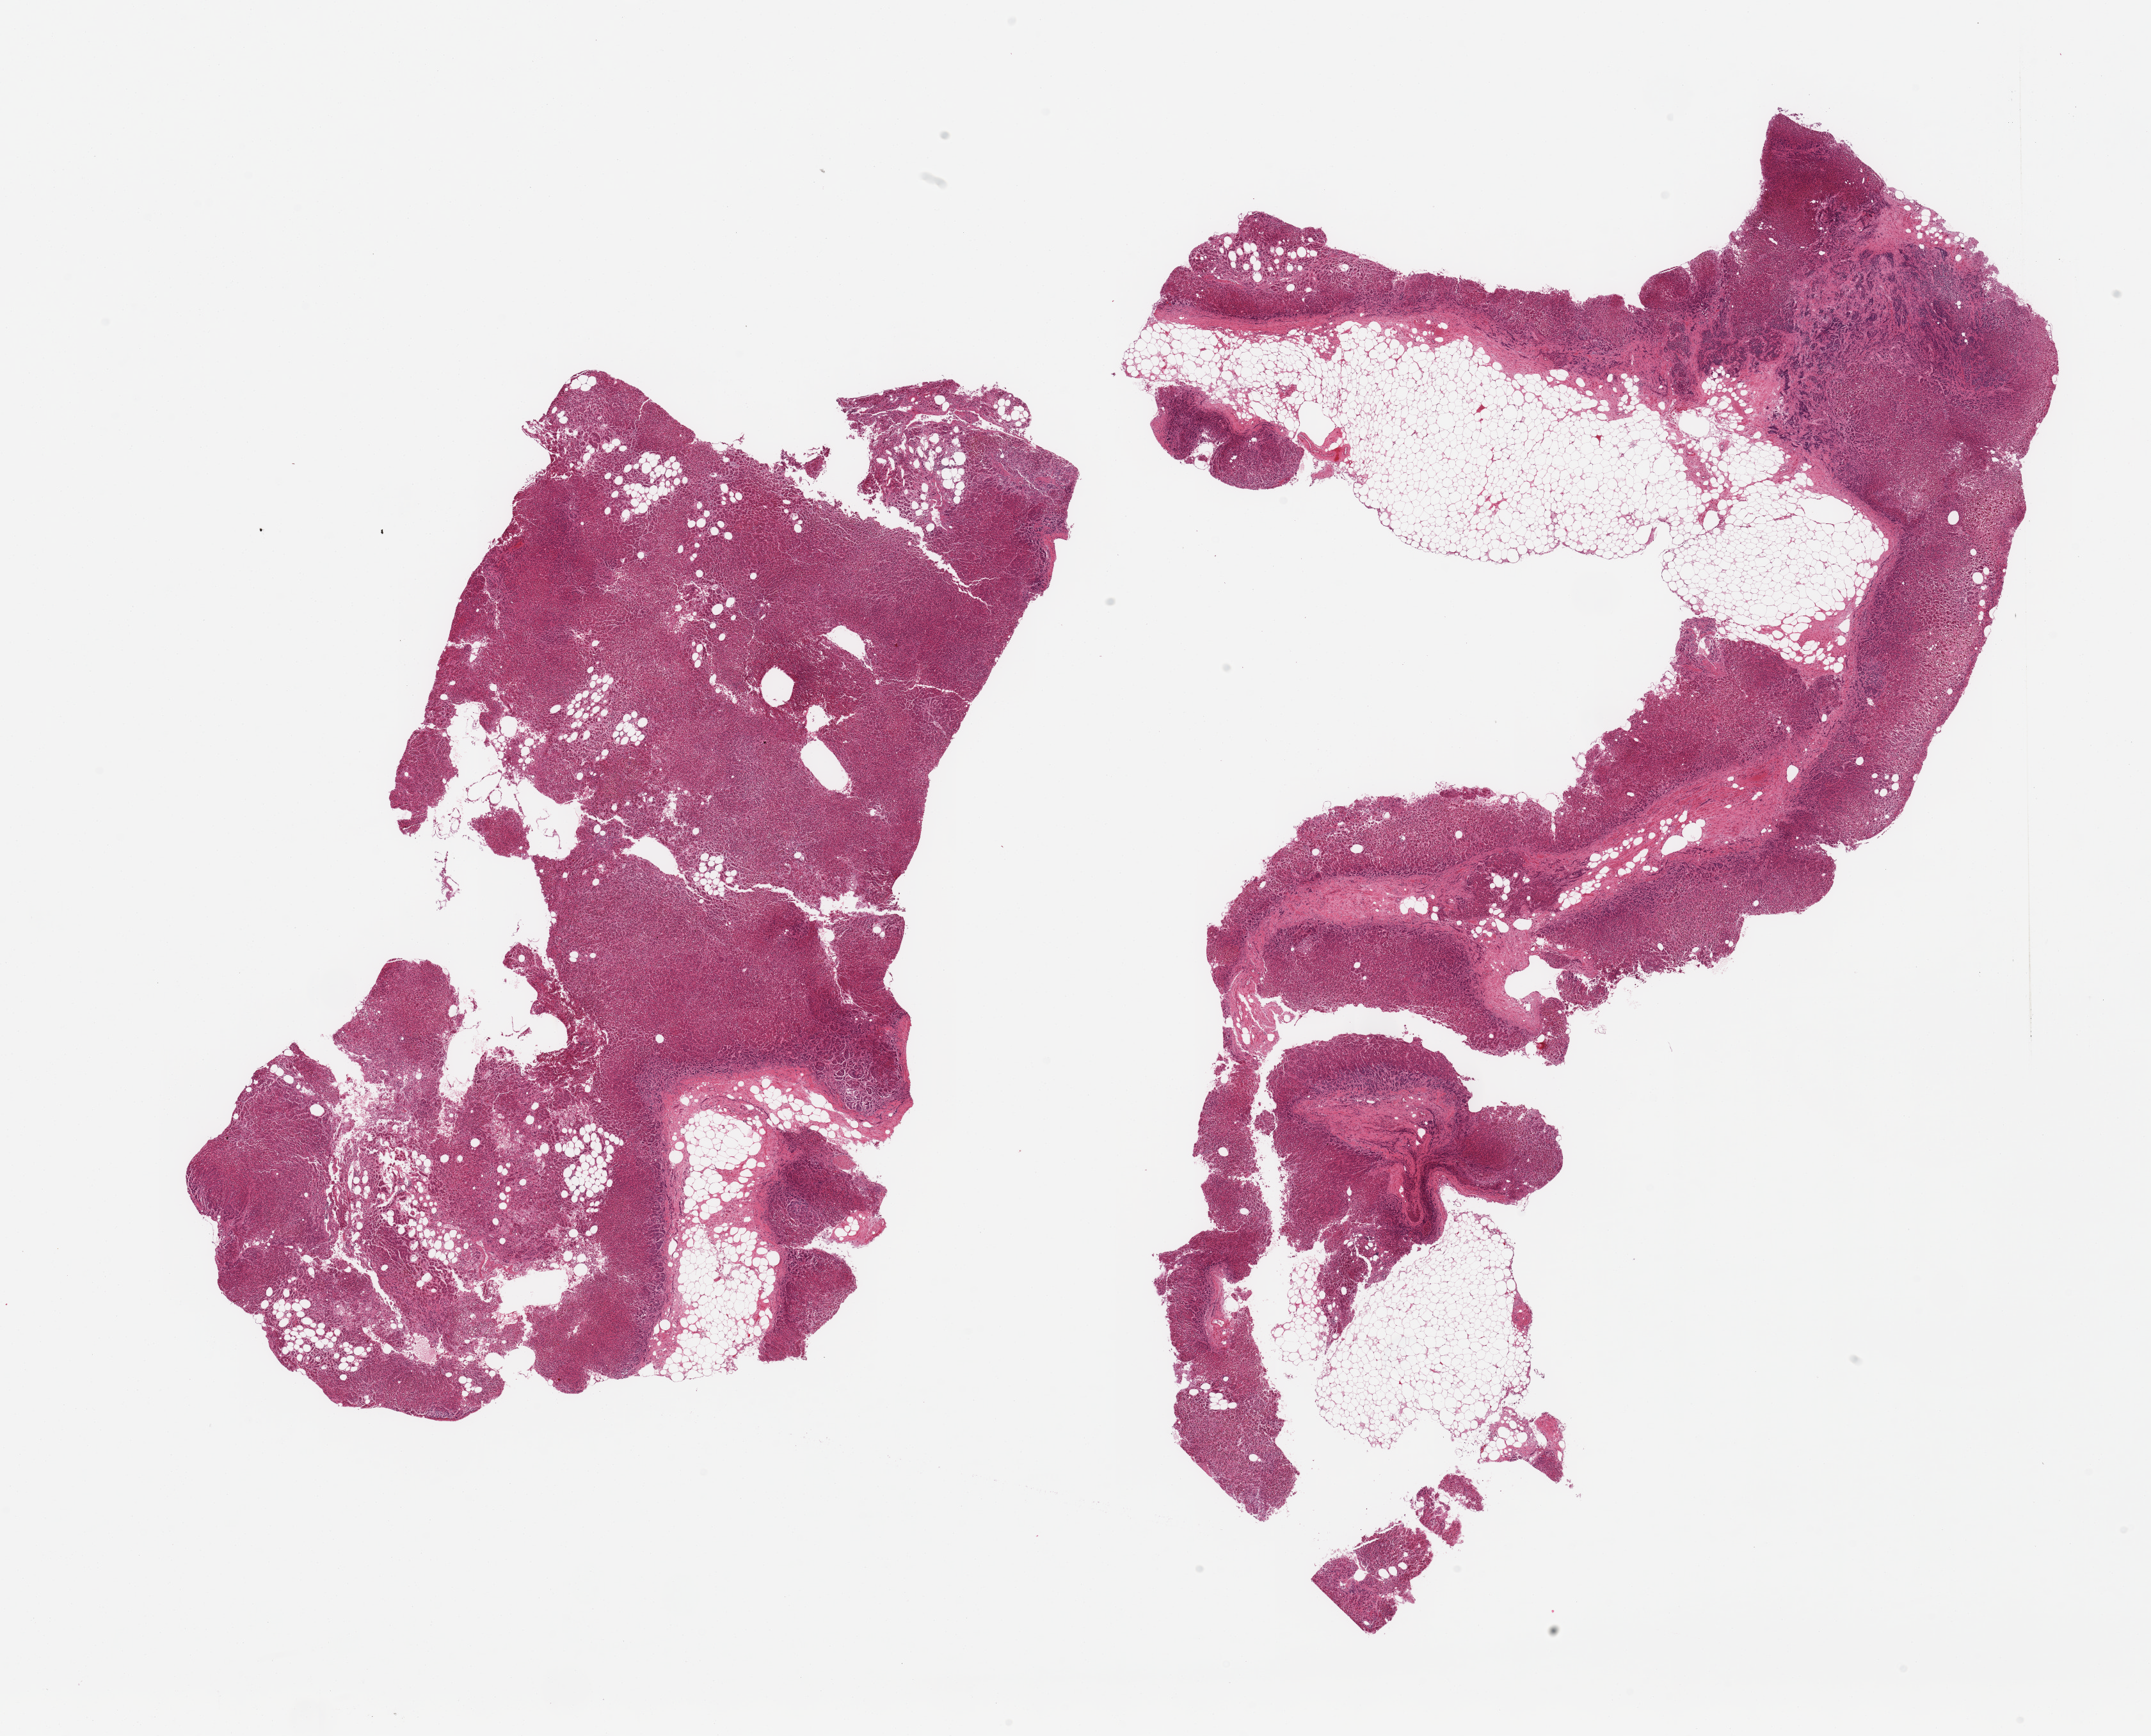
Haematoxylin and eosin whole-slide image, brightfield — low-resolution overview of the scanned area, about 26.6 x 21.5 mm; PAXgene-fixed, paraffin-embedded tissue; target tissue: adrenal gland; tissue donor sample. Donor sex: male.
* reviewer comment on this tissue sample: 2 pieces, cortex, ~20% adherent fat